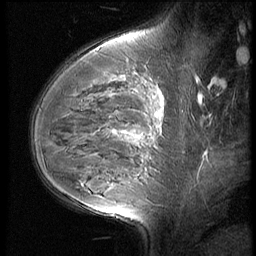
Breast MRI (dynamic contrast-enhanced), one sagittal slice. Slice 39 of 60 in the series (ordered by position). 3 images stored at this slice position (order not interpretable as contrast timing). 1.5 T. TE 4.2 ms, TR 9 ms. 256 × 256 image matrix. Patient: female, 35 years. From the clinical record (not read from this slice): setting: breast cancer imaged before/during neoadjuvant chemotherapy; receptor status: HR-positive, HER2-negative.
Annotated regions visible in this slice (semi-automatically segmented with operator editing):
- analysis volume of interest (the breast-tissue region the enhancement analysis was run in; not a lesion): bounding box <56,58,176,202> (left, top, right, bottom; pixels)
- tumour enhancement mask (voxels above the 140 % enhancement threshold inside the analysis volume of interest): <157,114,160,116>